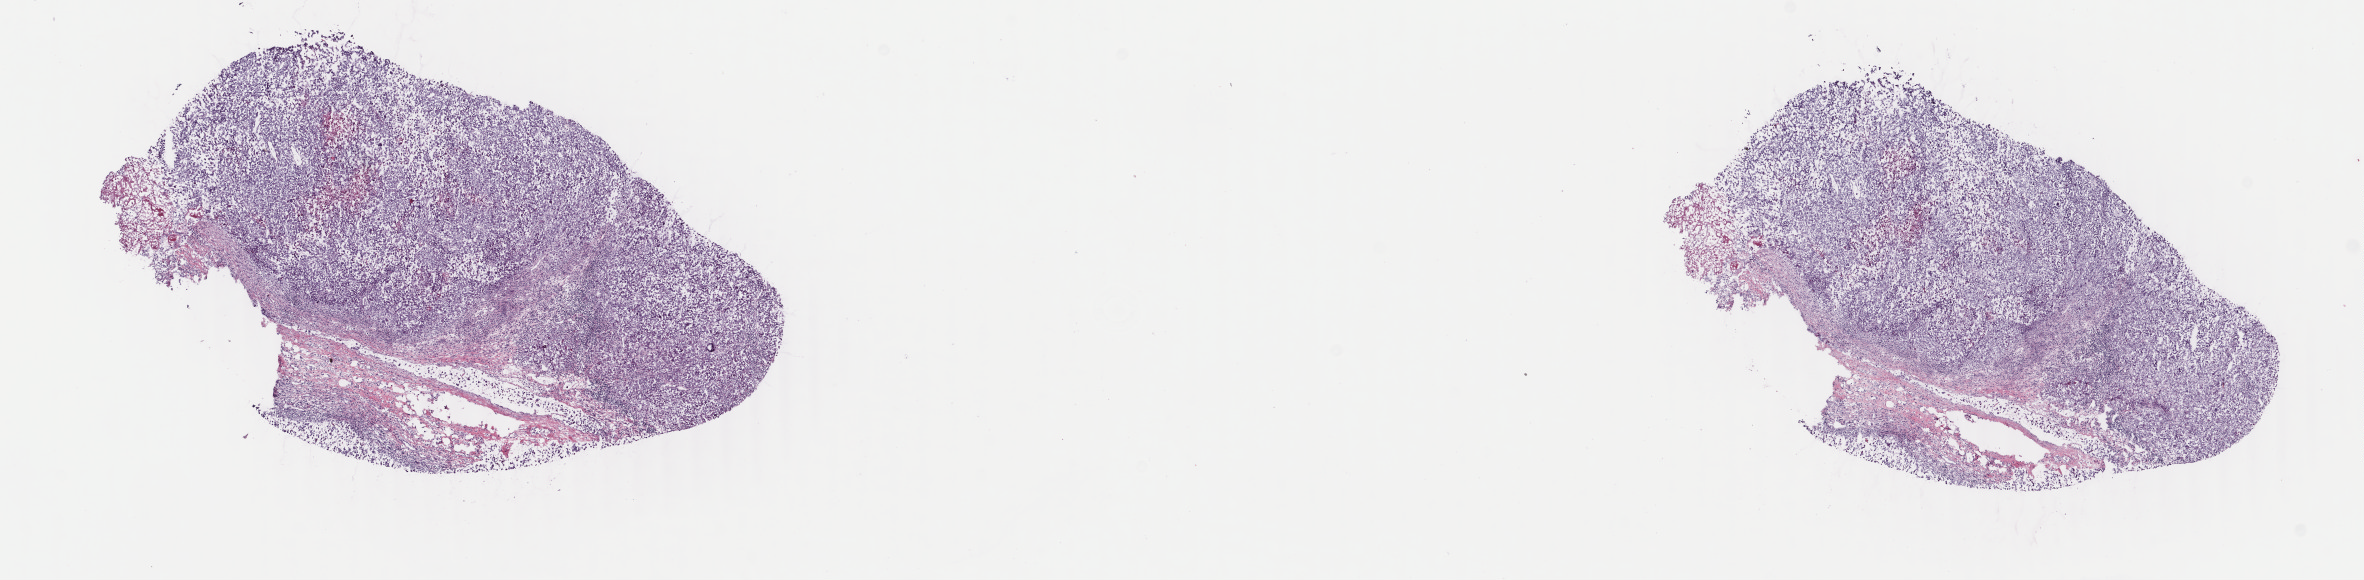
Whole-slide histology image, H&E, whole scanned area (about 18.8 x 4.6 mm, slide scanned at 40x) shown as a low-resolution overview; frozen section from the top of the tissue portion; metastatic tumour sample, sampled site: lymph nodes of axilla or arm. Female, age 62 years at initial diagnosis. Slide review estimates, as recorded: tumour cells 70%, tumour nuclei 70%, normal cells 0%, stromal cells 25%, necrosis 5%. Inflammatory infiltration, as recorded: lymphocyte infiltration 5%, monocyte infiltration 2%, neutrophil infiltration 2%.
- this section: metastatic tumour tissue
- patient diagnosis: Malignant melanoma, NOS